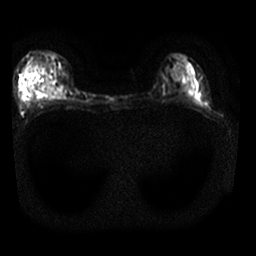
Breast MRI, one axial slice; position 14 of 25 along the scan axis; diffusion-weighted series; image 2 of 4 stored at this slice position (different b-values; order by instance number); 1.5 T; 4 mm slice thickness; 256 × 256 image matrix, field of view 310 × 310 mm. Female patient.
Annotated regions visible in this slice (expert manual segmentation):
- tumour on diffusion-weighted imaging: bounding box <47,88,51,92> (left, top, right, bottom; pixels)